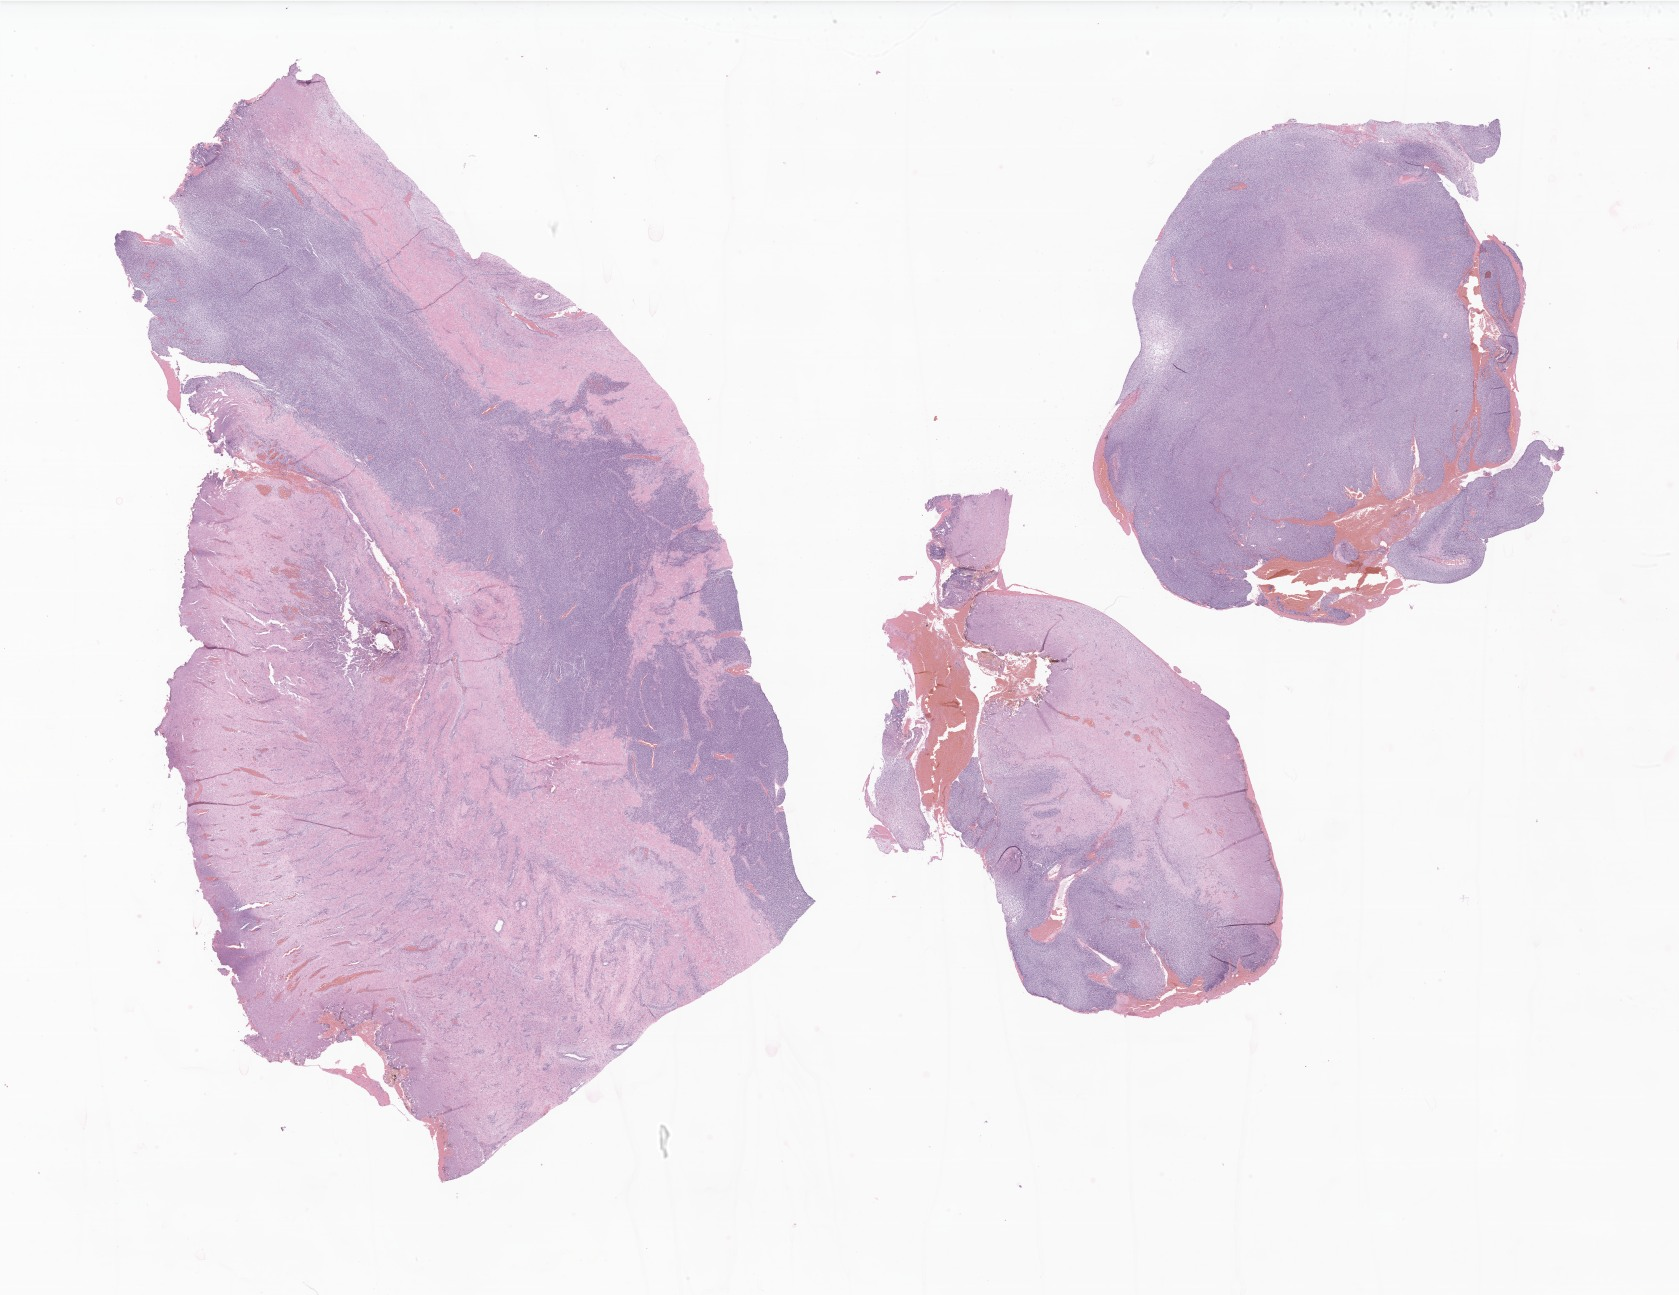
H&E whole-slide image of tumor tissue from the thorax, low-resolution overview of the scanned area, about 28.3 x 21.8 mm. FFPE section. Patient male; age 292 months (24 years 4 months).
Recorded diagnosis: Malignant peripheral nerve sheath tumor, NOS.